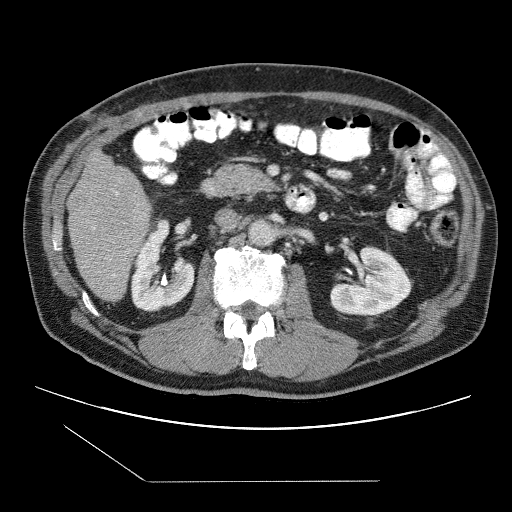
Contrast-enhanced abdominal CT (liver protocol), one axial slice. Position 31 of 109 along the scan axis. 120 kVp. One of 2 acquisitions stored at this slice position. Soft-tissue window (W 400 / L 40 HU). 512 × 512 image matrix, field of view 400 × 400 mm. Case-level facts recorded for this patient, not image findings: diagnosis: hepatocellular carcinoma (patient treated with transarterial chemoembolisation; whether this scan precedes or follows treatment is not stated here); TNM stage (as recorded): Stage-IIIB; Child-Pugh class: A; tumour nodularity: multinodular.
Structures marked on this image (semi-automatically segmented with operator editing):
- liver parenchyma outside the tumour (the mass and vessels are separate outlines, so this box may not span the whole liver): bounding box <66,149,152,300> (left, top, right, bottom; pixels)
- liver vessels: <112,193,118,277>